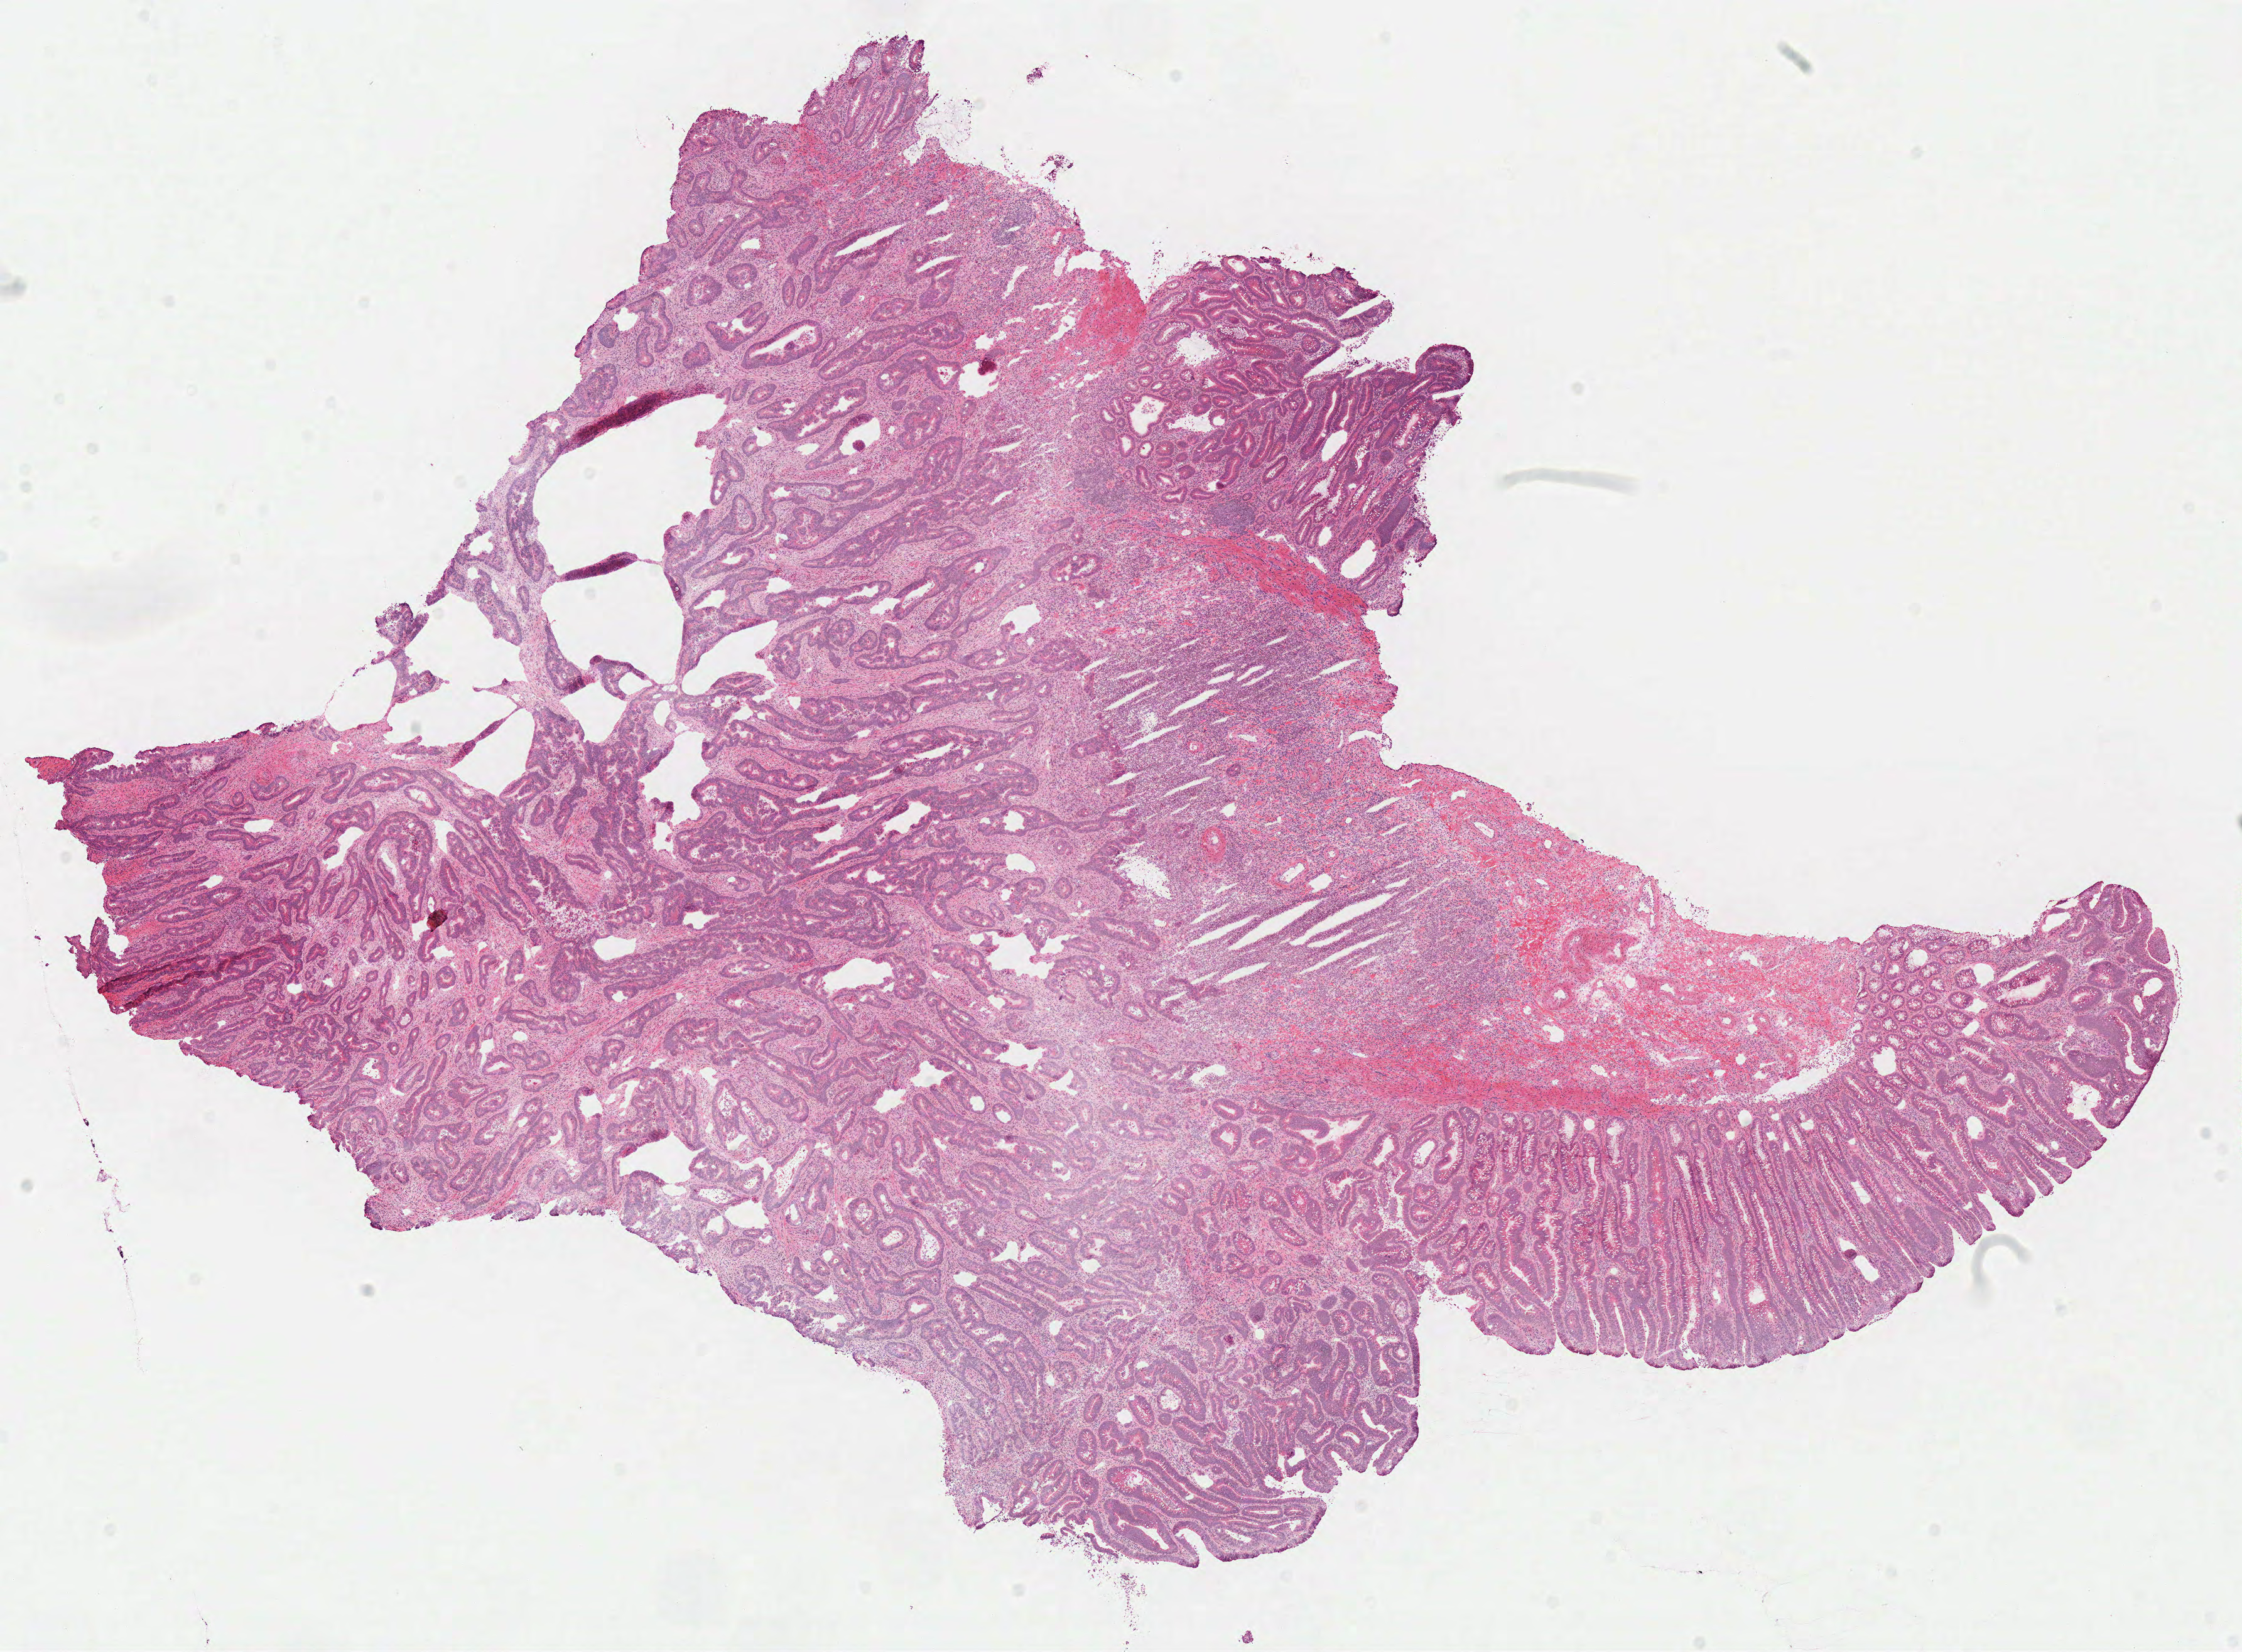
Hematoxylin and eosin (H&E) stained whole-slide image — shown as a low-resolution overview of the whole scanned area (about 14.1 x 10.4 mm, acquisition: 40x scan). Frozen section. Primary tumour sample from the colon. Patient: female, age at initial diagnosis 72 years. Pathologist review of this section (percent, as recorded): tumour cells 65%, tumour nuclei 70%, normal cells 15%, stromal cells 15%, necrosis 5%.
- TNM: T2 N0 M0
- diagnosis: Adenocarcinoma, NOS (descending colon)
- lymph nodes positive (case pathology): 0 of 12 examined
- AJCC pathologic stage: I